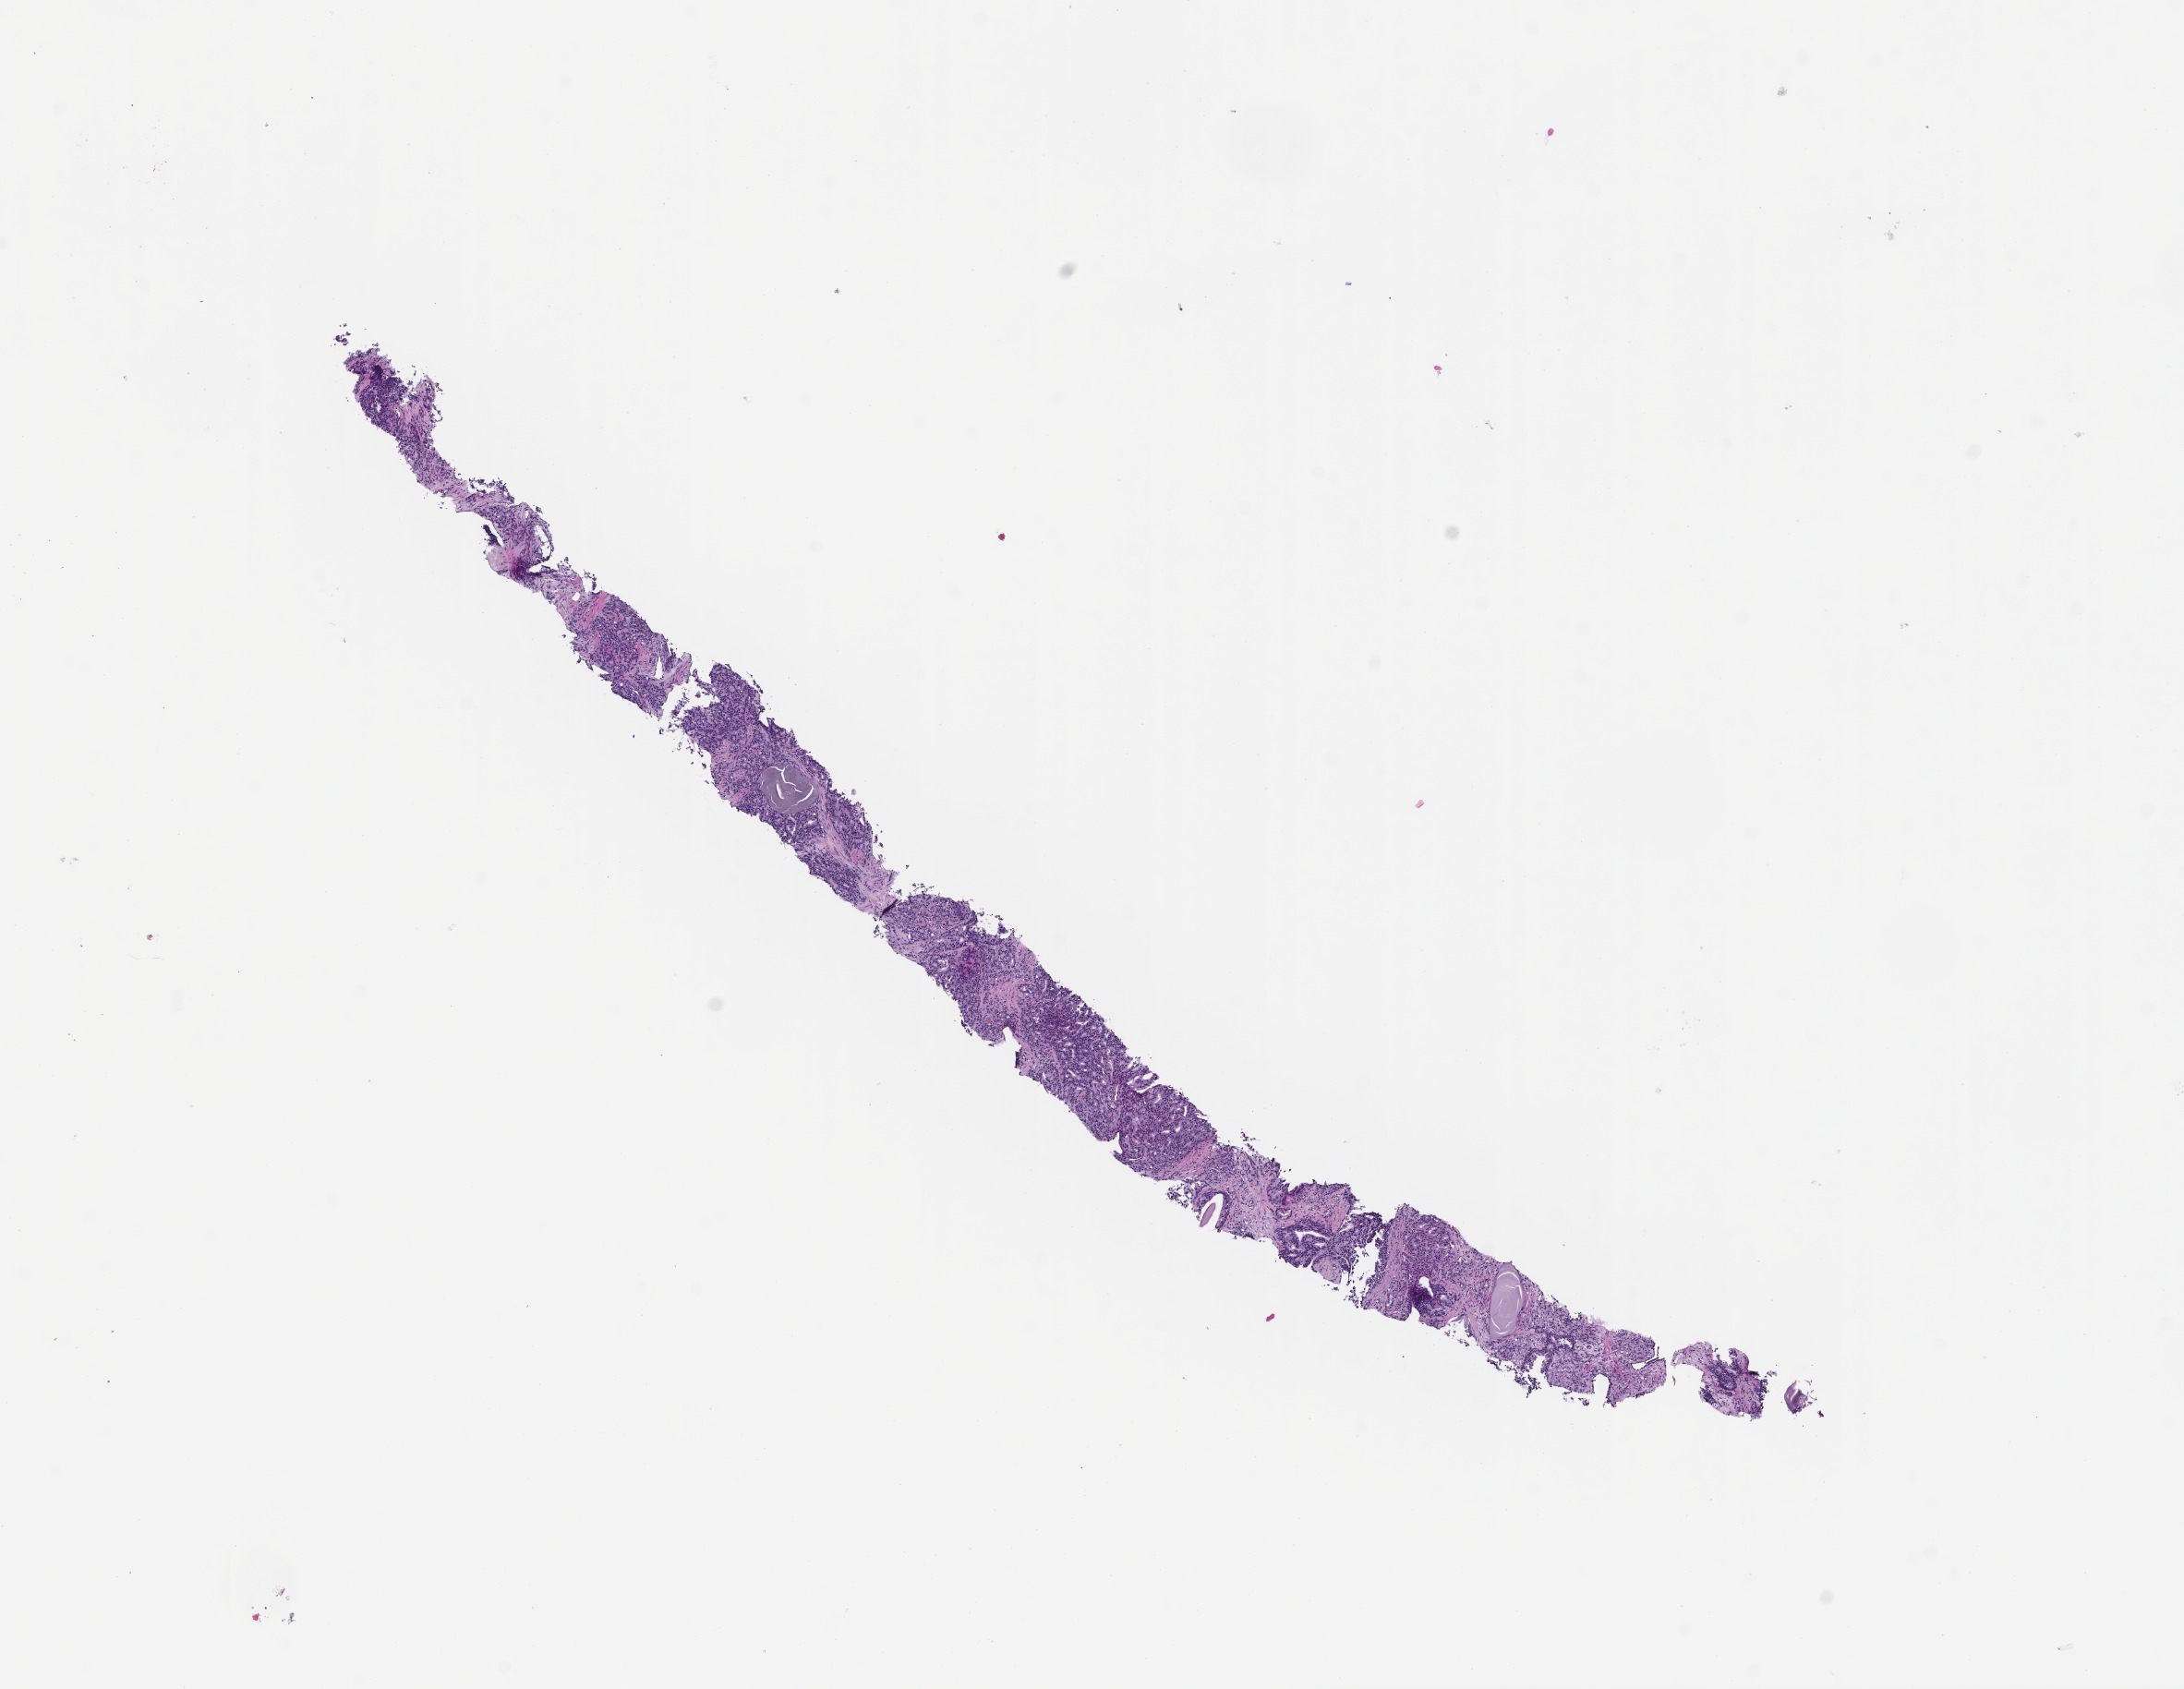
H&E whole-slide image — shown as a low-resolution overview of the whole scanned area (about 9.5 x 7.4 mm); formalin-fixed paraffin-embedded section; tissue site: prostate; archival tissue. Patient sex: male.
This section: primary tumour tissue. Diagnosis: Prostate Carcinoma.